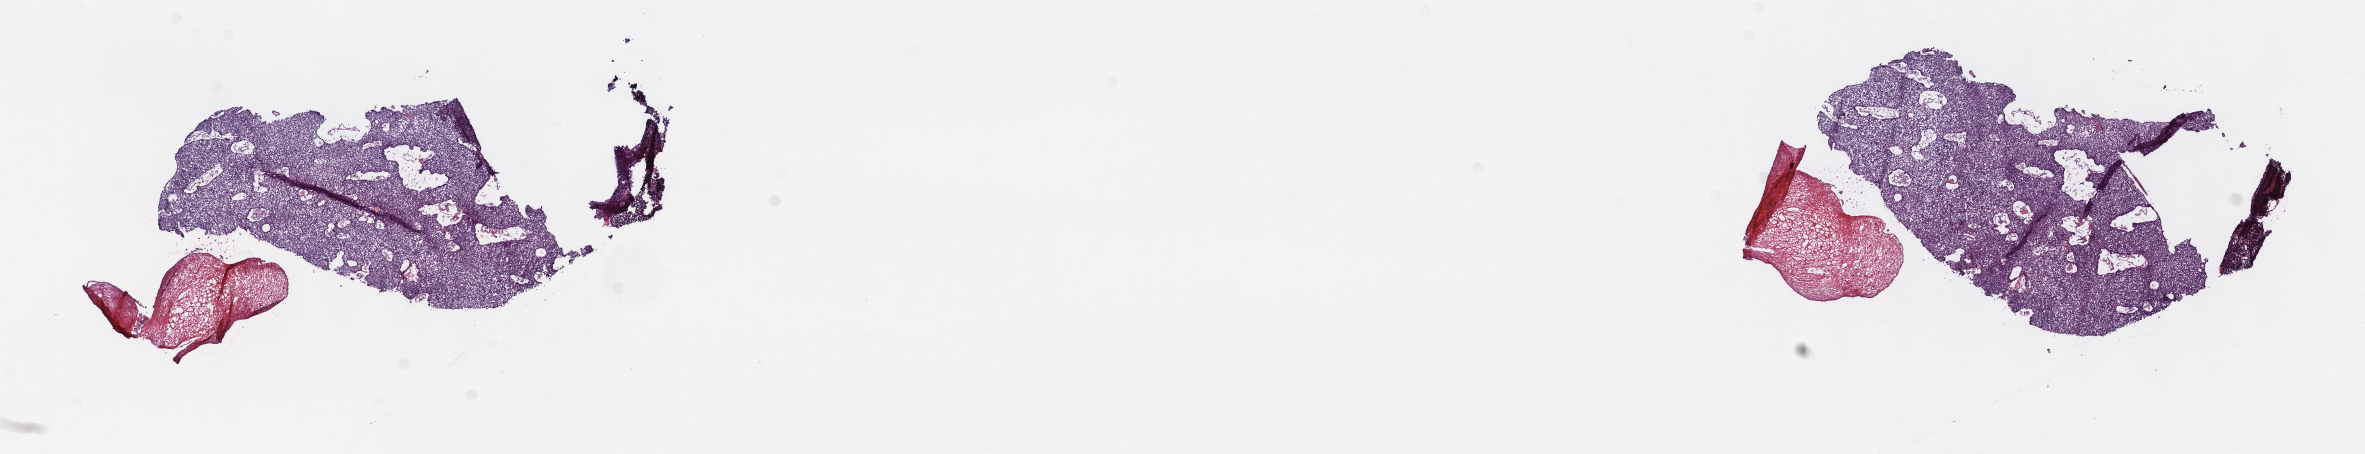
Digitized H&E tissue section (whole slide) — whole scanned area (about 19.1 x 3.7 mm, acquisition: 40x scan) shown as a low-resolution overview. Frozen section from the top of the tissue portion. Thymus, primary tumour sample. Female, age 43 years at initial diagnosis. Slide review estimates, as recorded: tumour cells 100%, tumour nuclei 80%, normal cells 0%, stromal cells 0%, necrosis 0%. Infiltration values recorded for this section: lymphocyte infiltration 2%, monocyte infiltration 0%, neutrophil infiltration 0%.
* histologic diagnosis: Thymoma, type B2, malignant